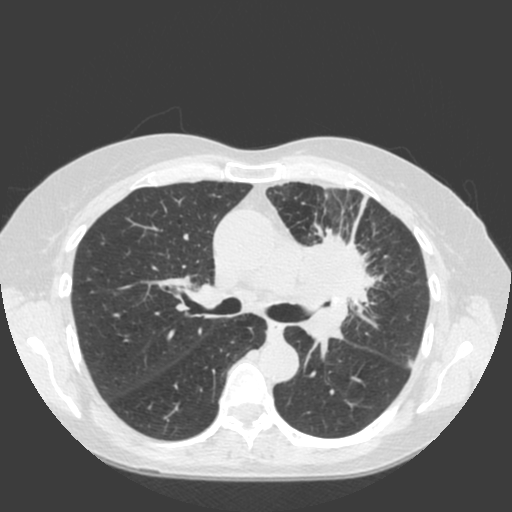
Low-dose screening chest CT, one axial slice. Slice 119 of 184 in the series (ordered by position). Lung window (W 1500 / L -600 HU). 2 mm slice thickness. 512 × 512 image matrix, field of view 350 × 350 mm.
Outlined on this slice (outlined manually by an expert reader):
- lesion 1 (tumor, hilum of left lung): bounding box <295,231,376,355> (left, top, right, bottom; pixels)